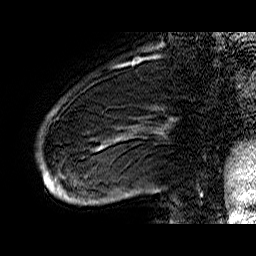
Breast MRI (dynamic contrast-enhanced), one sagittal slice; position 10 of 60 along the scan axis; dynamic contrast-enhanced series, time point 2 of 6 at this slice position (early post-contrast); 1.5 T; TE 6.4 ms, TR 32.9 ms; 4 mm slice thickness; 256 × 256 image matrix, field of view 200 × 200 mm. Female patient. From the clinical record (not read from this slice): setting: breast cancer imaged before/during neoadjuvant chemotherapy; receptor status: HR-positive, HER2-negative.
Structures marked on this image (semi-automatically segmented with operator editing):
- analysis volume of interest (the breast-tissue region the enhancement analysis was run in; not a lesion): bounding box (x1, y1, x2, y2) in pixels: (42, 74, 176, 206)
- tumour enhancement mask (voxels above the 100 % enhancement threshold inside the analysis volume of interest): (42, 111, 122, 201)